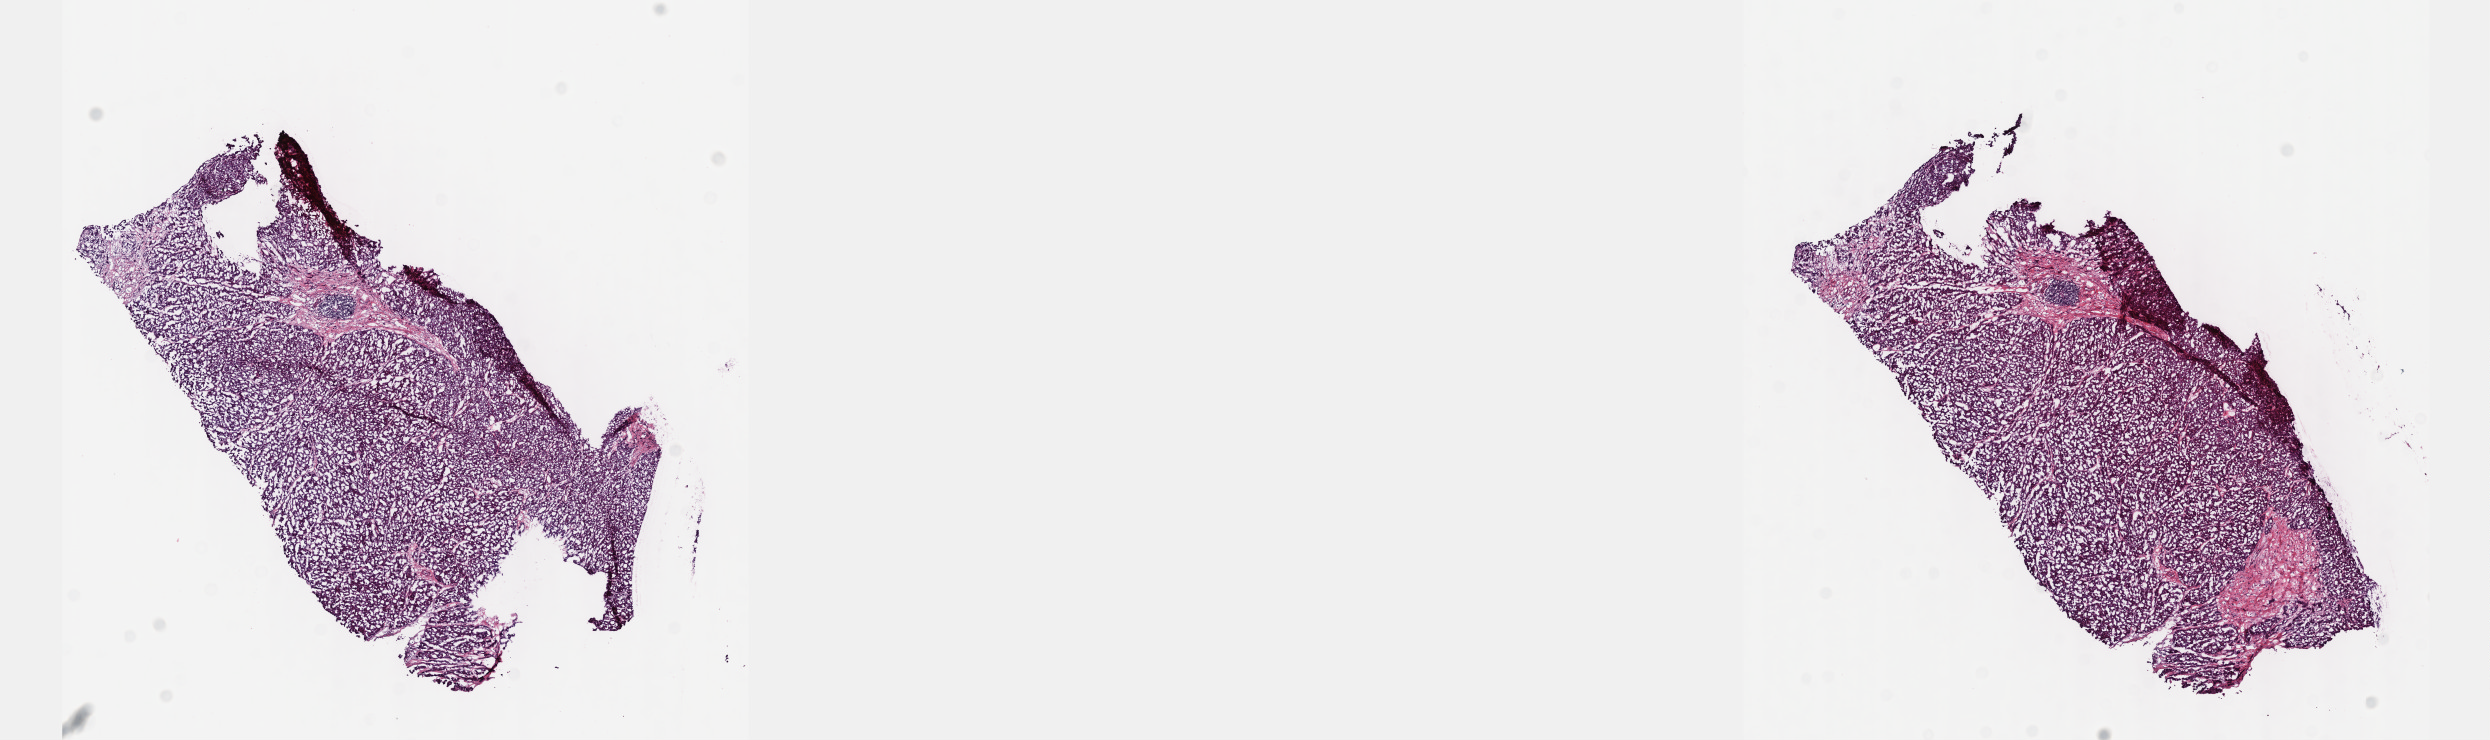
H&E whole-slide image, a low-resolution overview of the entire scanned area, about 20.1 x 6.0 mm (acquisition: 40x scan). Frozen section from the top of the tissue portion. Sample: primary tumour, liver. Male, age 59 years at initial diagnosis. Histologic grade: G3 (poorly differentiated). Slide review estimates, as recorded: tumour cells 100%, tumour nuclei 80%, normal cells 0%, stromal cells 0%, necrosis 0%. Inflammatory infiltration, as recorded: lymphocyte infiltration 2%, monocyte infiltration 0%, neutrophil infiltration 0%.
Histologic diagnosis: Hepatocellular carcinoma, NOS. AJCC pathologic stage: I (7th edition).